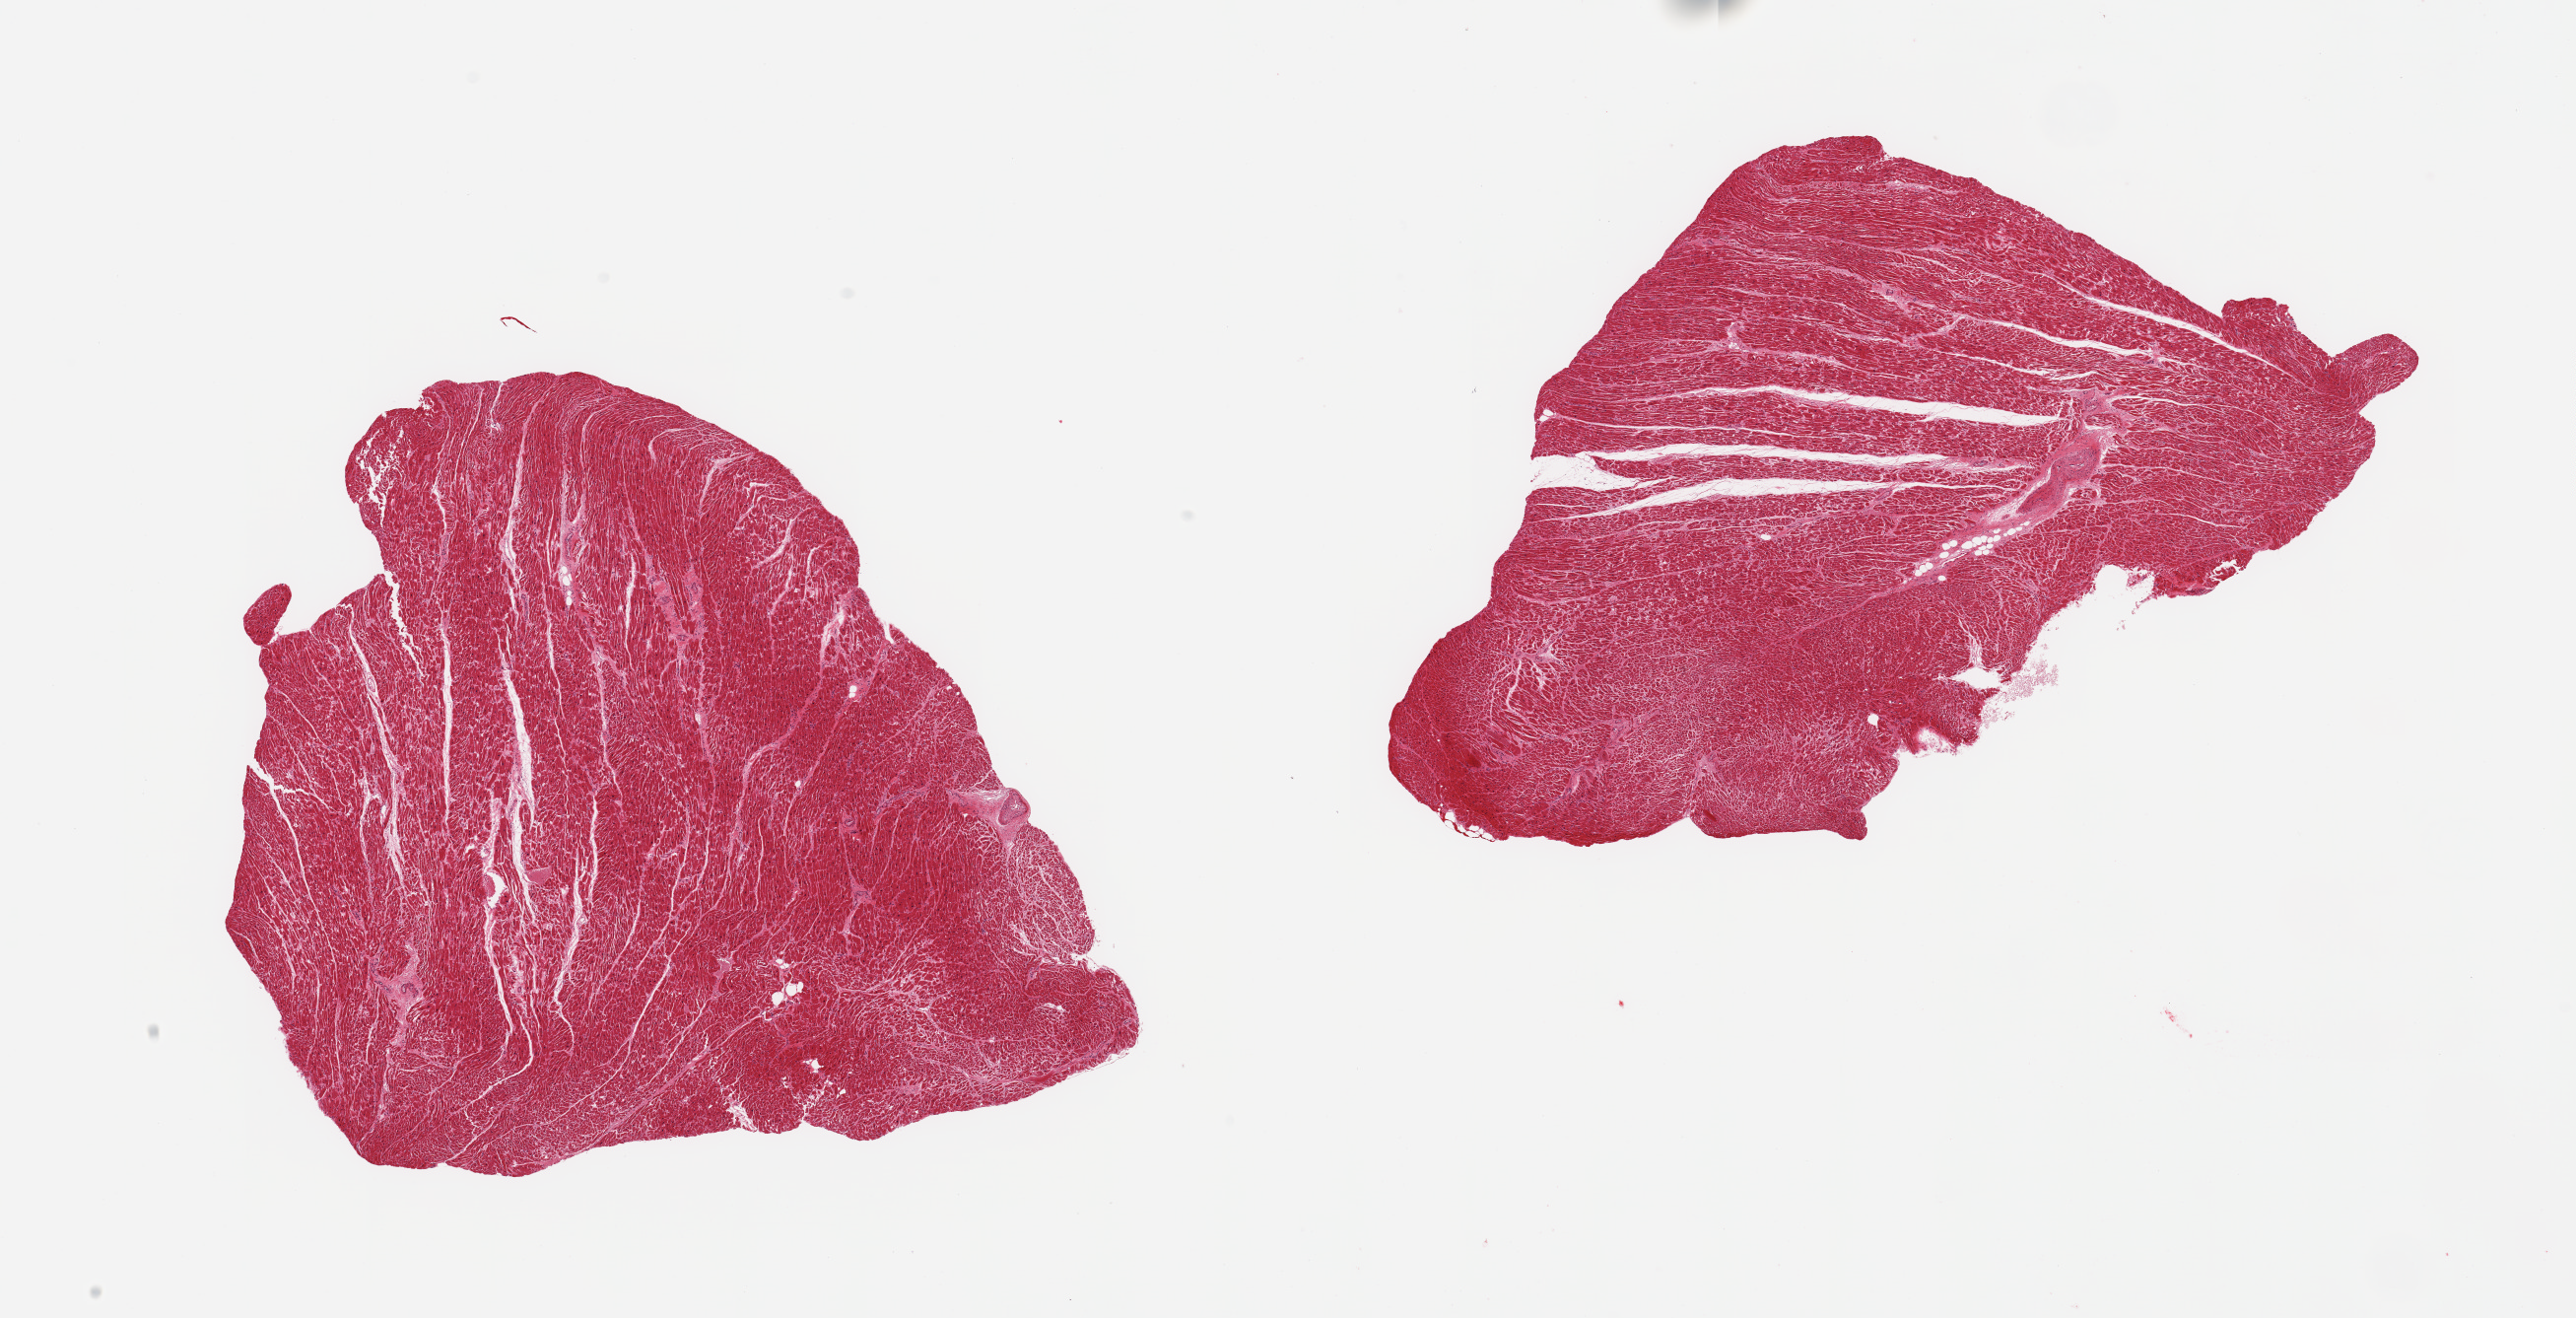
Whole-slide image, haematoxylin and eosin stain, brightfield, whole scanned area (about 20.7 x 10.6 mm, slide scanned at 20x) shown as a low-resolution overview, PAXgene-fixed, paraffin-embedded tissue, target tissue: heart, donor tissue sample. Donor: male.
Reviewer comment on this tissue sample: 2 pieces; some interstitial fibrosis.